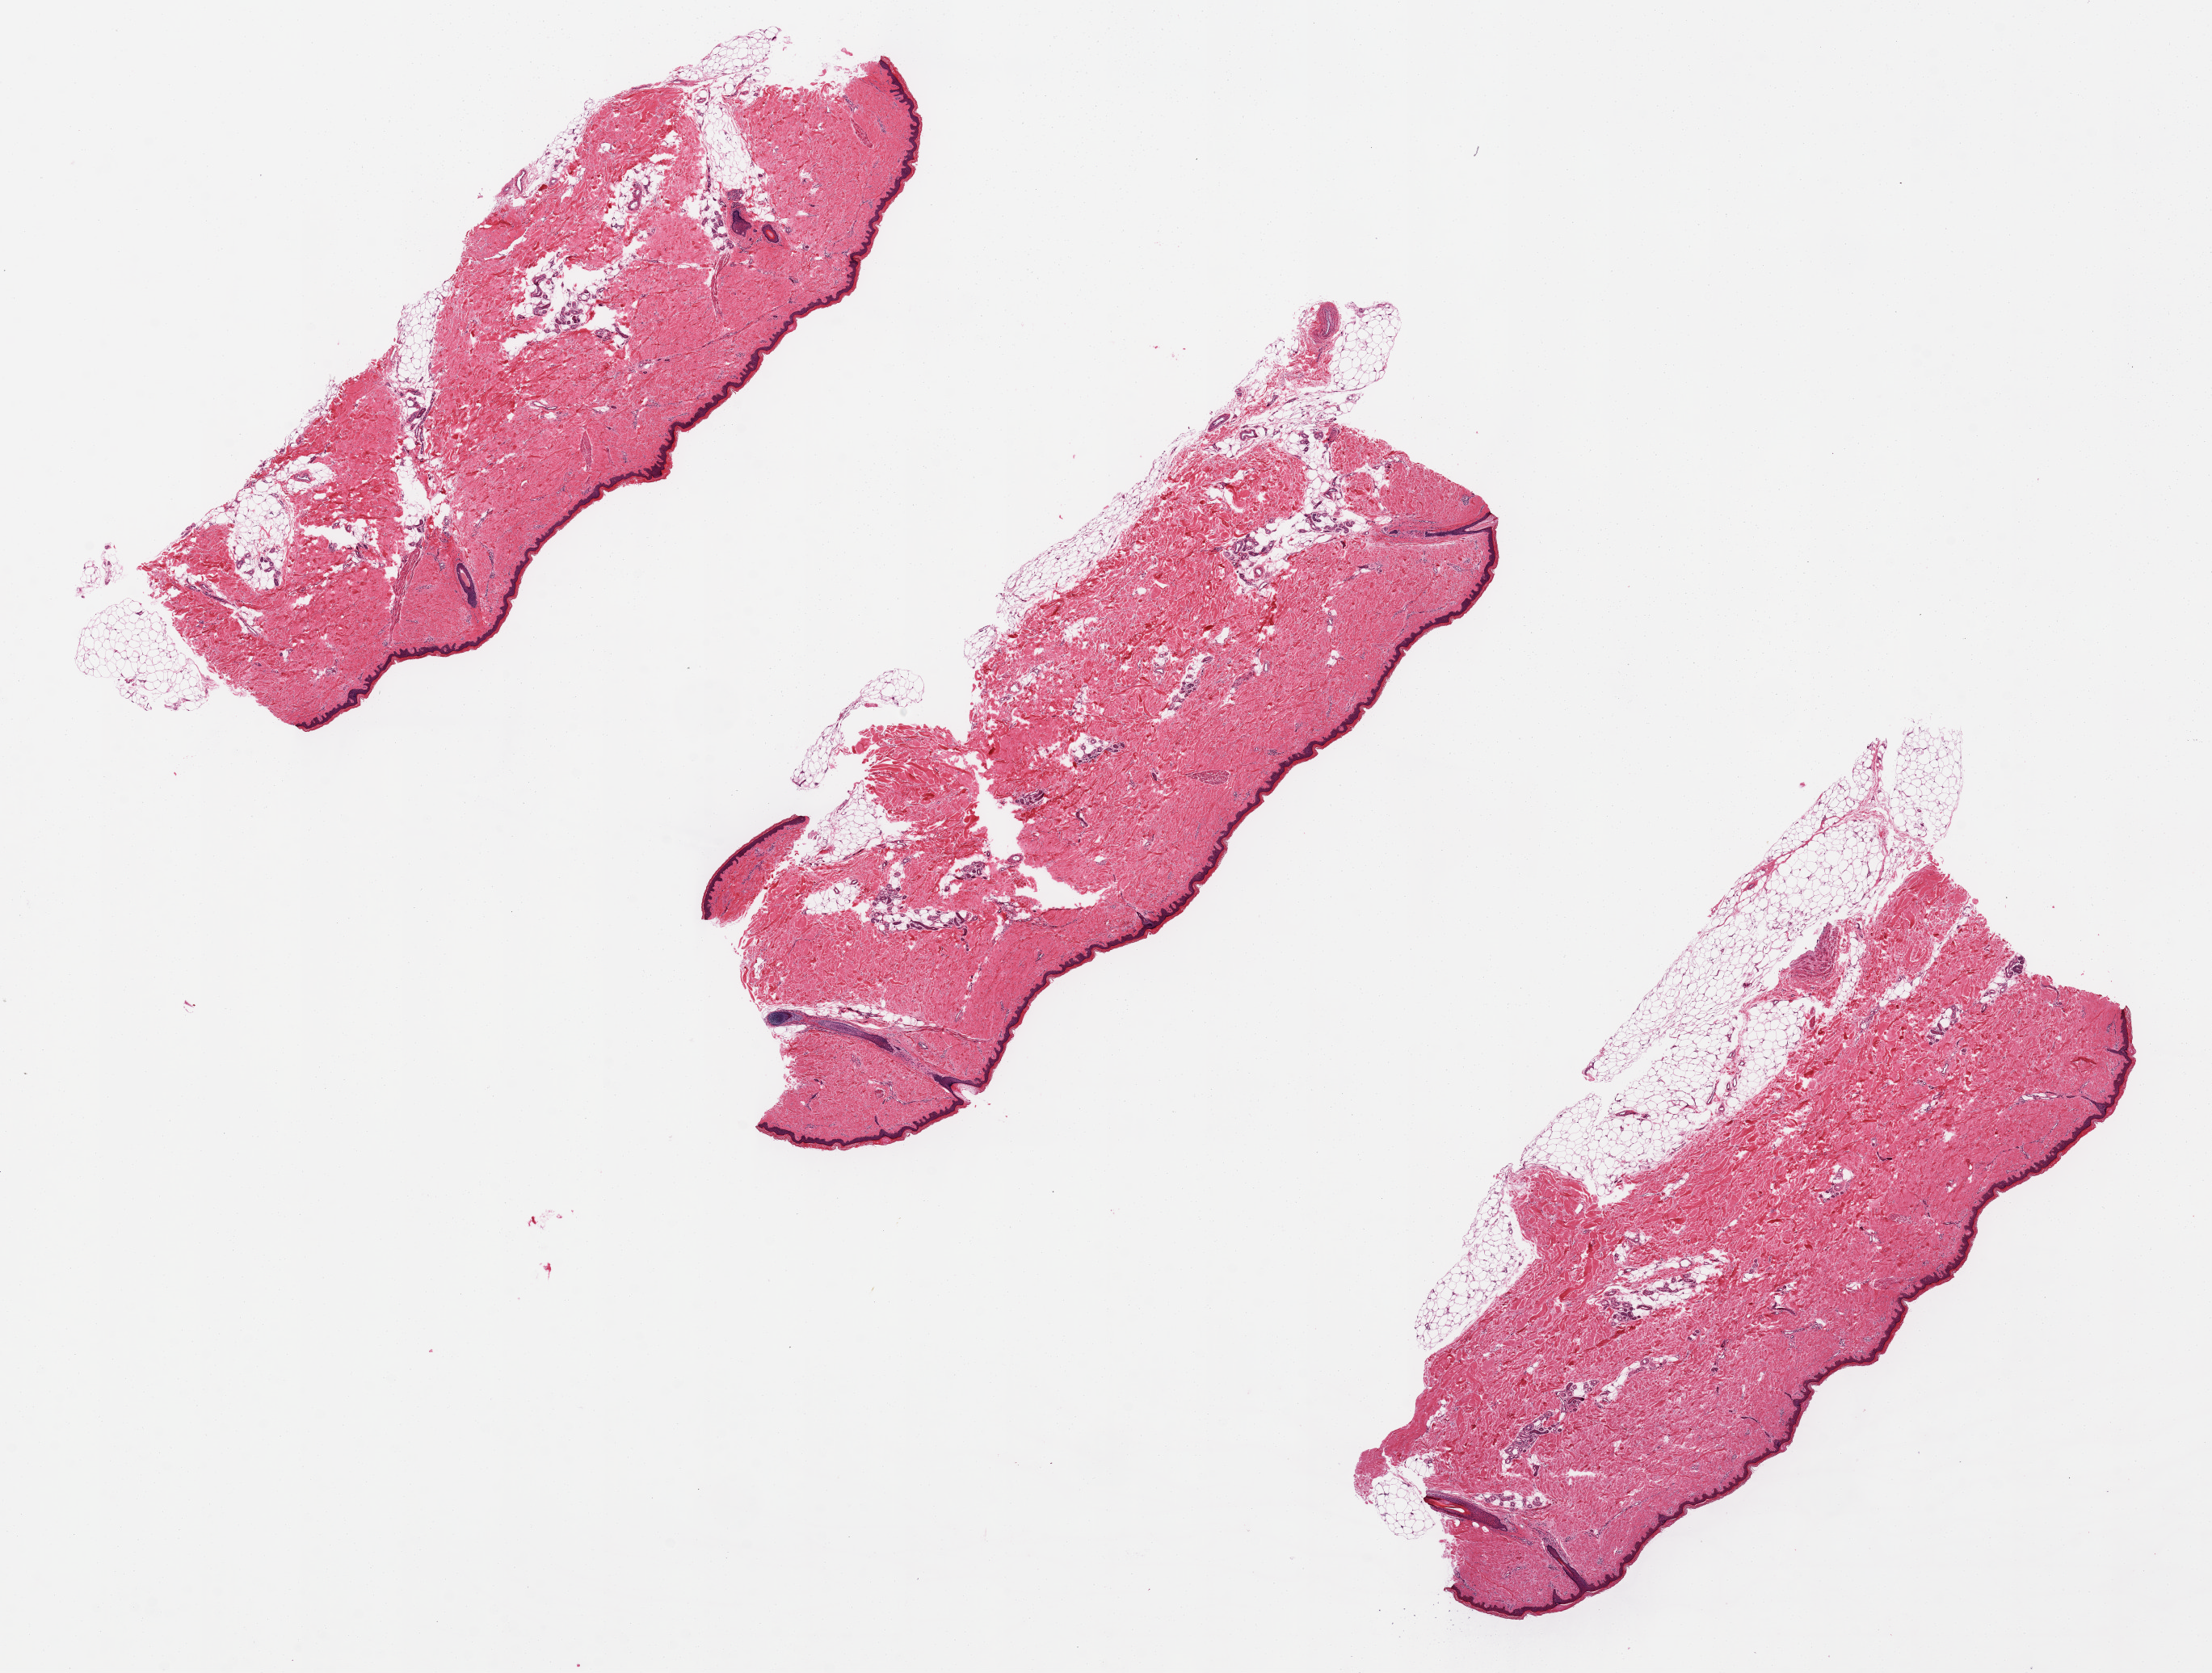
Digitized H&E-stained section, a low-resolution overview of the entire scanned area, about 21.7 x 16.4 mm, PAXgene-fixed, paraffin-embedded tissue, section of skin of lower leg (target tissue), tissue donor sample. Donor: female.
- pathologist's review note for this sample: 8.5x4mm. Epidermis 0.084mm